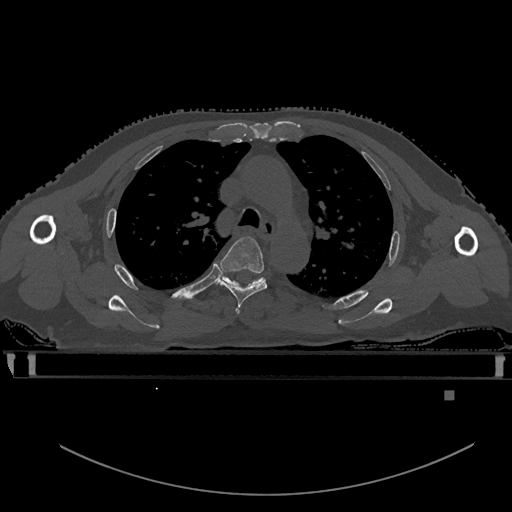
CT including the spine, one axial slice; position 396 of 969 along the scan axis; bone window (W 1800 / L 400 HU); 0.5 mm slice thickness; 512 × 512 image matrix, field of view 456 × 456 mm. Male patient, age 82 years. From the clinical record (not read from this slice): primary cancer: prostate; vertebrae with lytic lesions (as recorded): T11, T9, T8, T2.
Structures marked on this image (semi-automatic segmentation, software-assisted and operator-edited):
- T3 vertebra: bounding box [x1, y1, x2, y2] px = [236, 310, 240, 314]
- T4 vertebra: [217, 236, 268, 310]
- T5 vertebra: [218, 272, 263, 285]